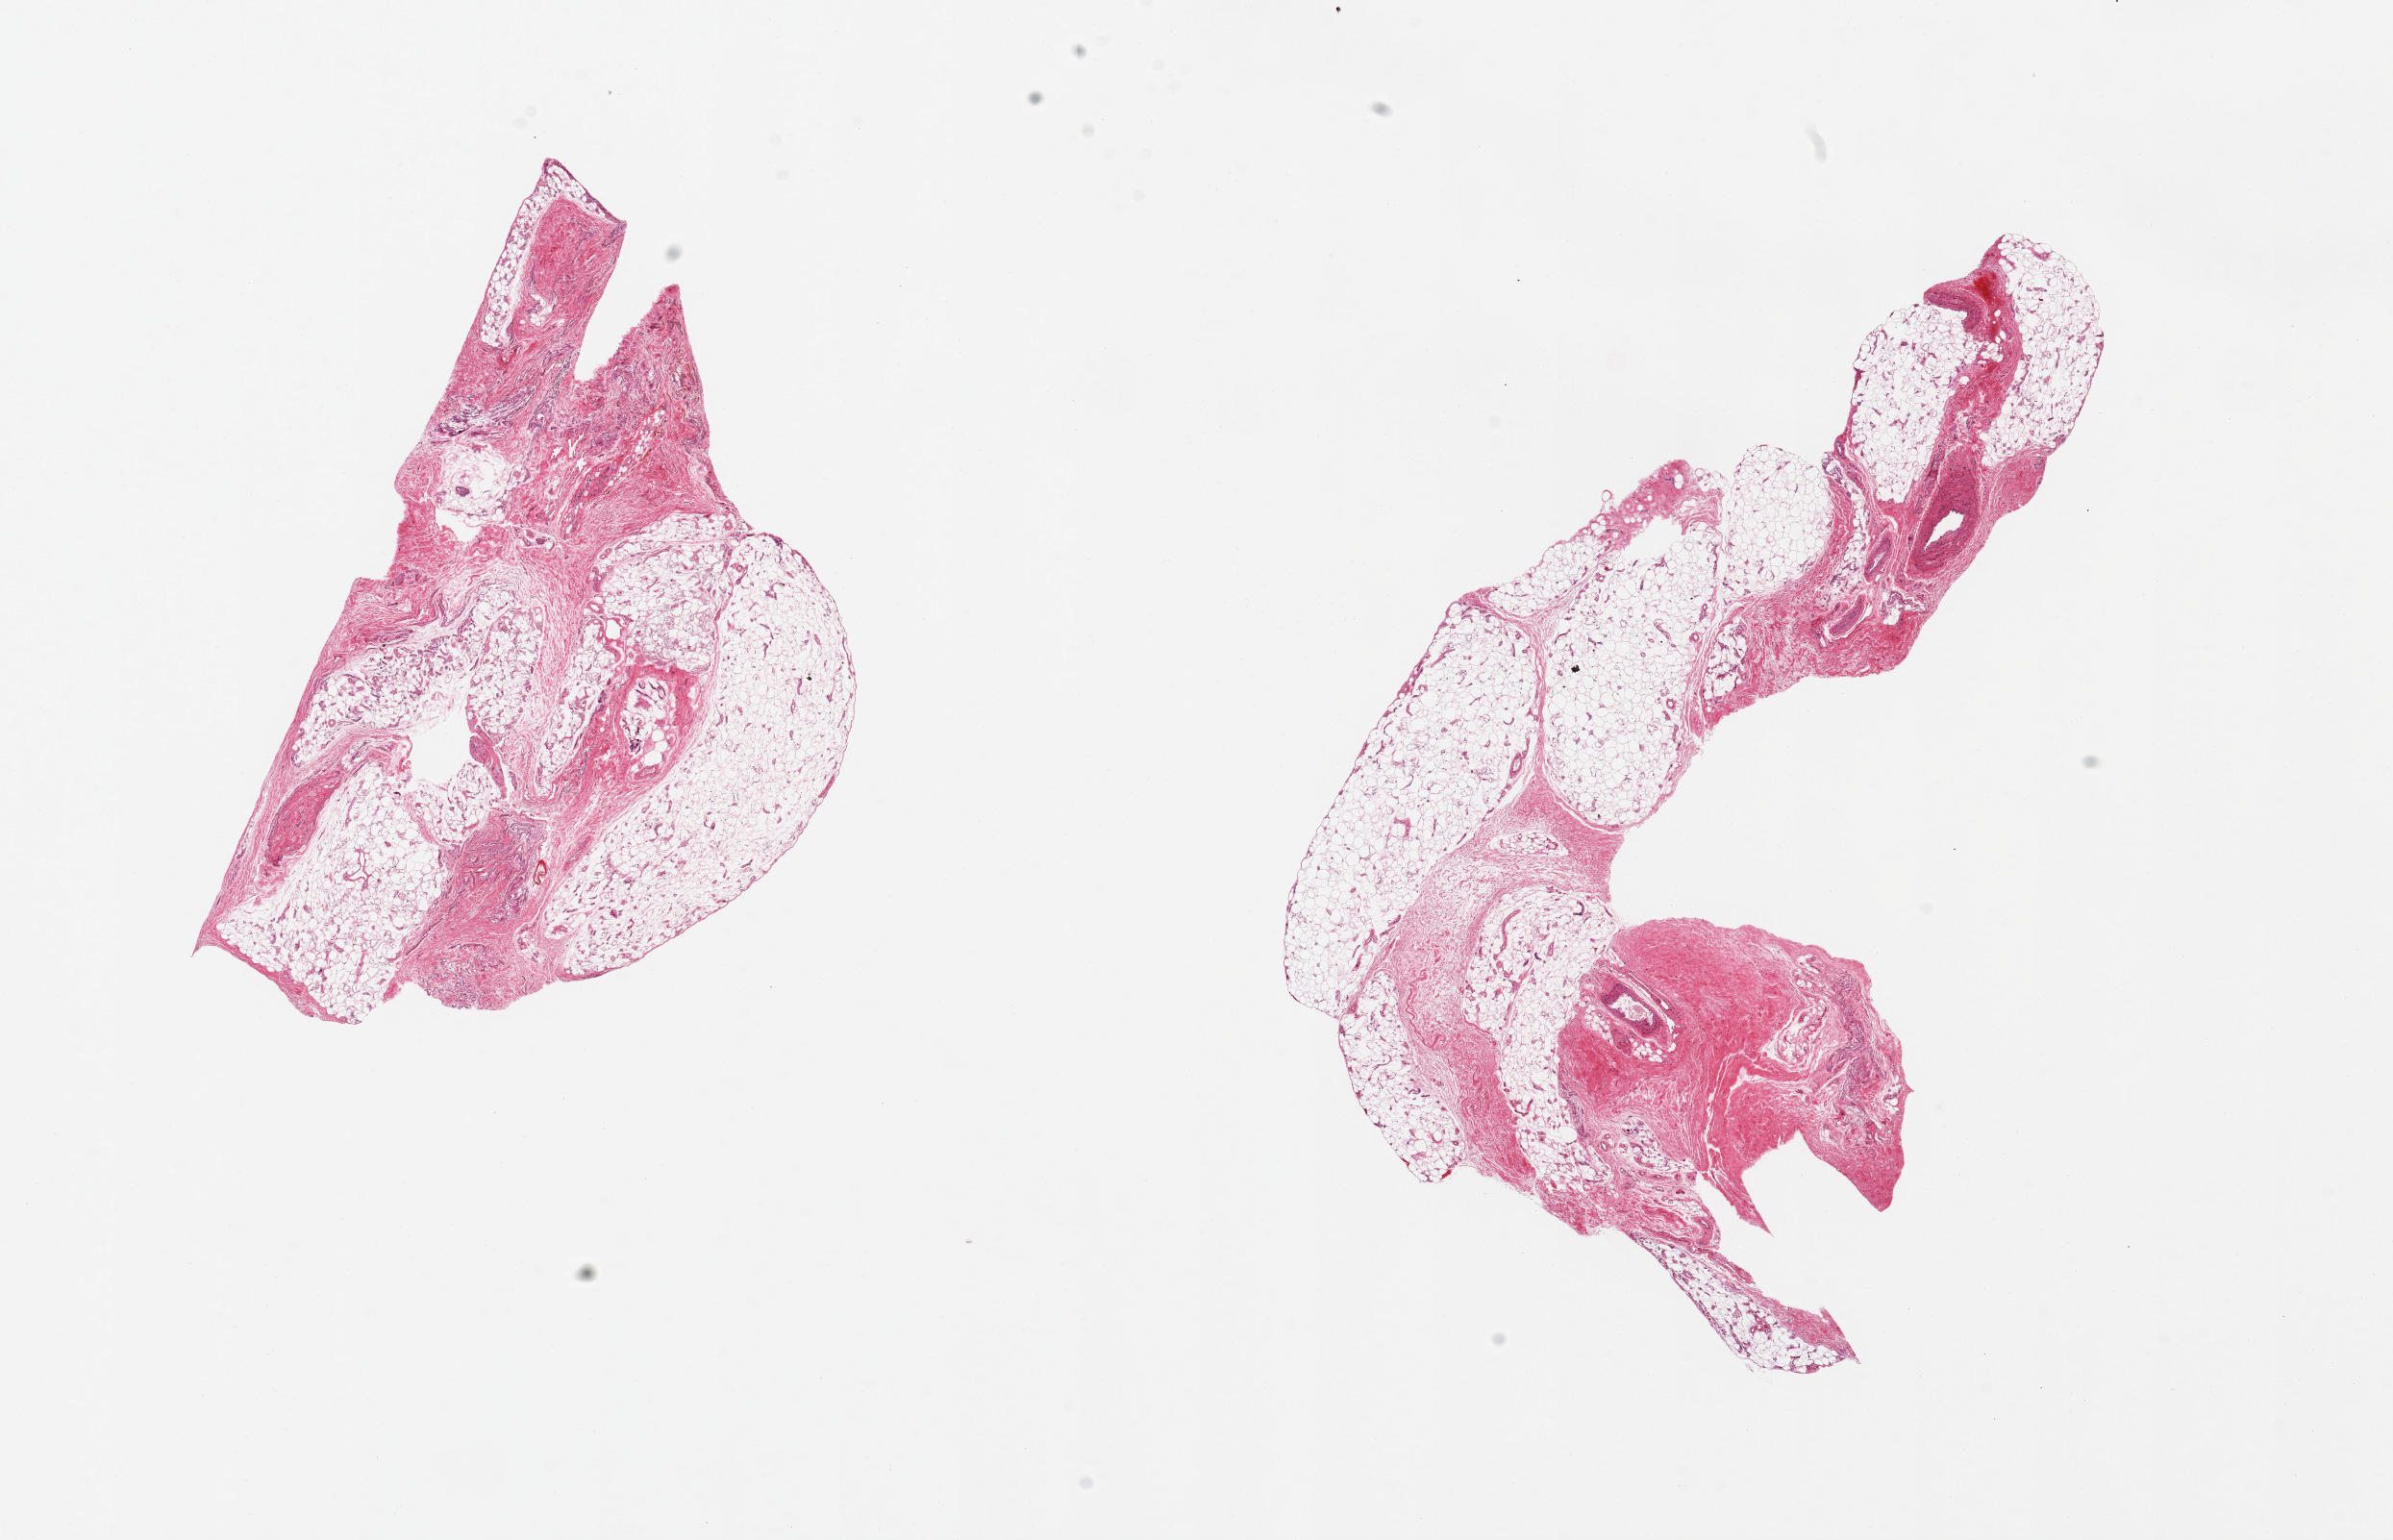
Digitized H&E-stained section, whole scanned area (about 19.7 x 12.7 mm, from a 20x scan) shown as a low-resolution overview. PAXgene-fixed paraffin-embedded (PFPE) section. Section of adipose tissue (target tissue). Tissue donor sample. Donor: male.
Review note (as recorded): 2pieces, ~7x6mm. Mixed fibrous-adipose tissues.